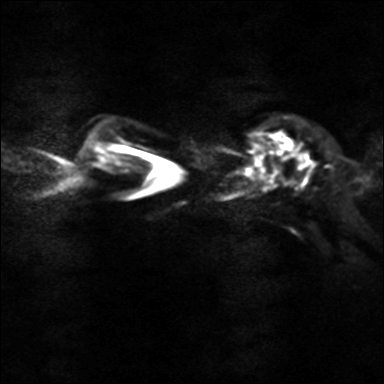
Breast MRI, one axial slice; slice 27 of 40 in the series (ordered by position); diffusion-weighted series; image 2 of 4 stored at this slice position (different b-values; order by instance number); 3 T; 4 mm slice thickness; 384 × 384 image matrix. Female patient.
Annotated regions visible in this slice (outlined manually by an expert reader):
- tumour on diffusion-weighted imaging: bounding box (x1, y1, x2, y2) in pixels: (300, 151, 308, 158)